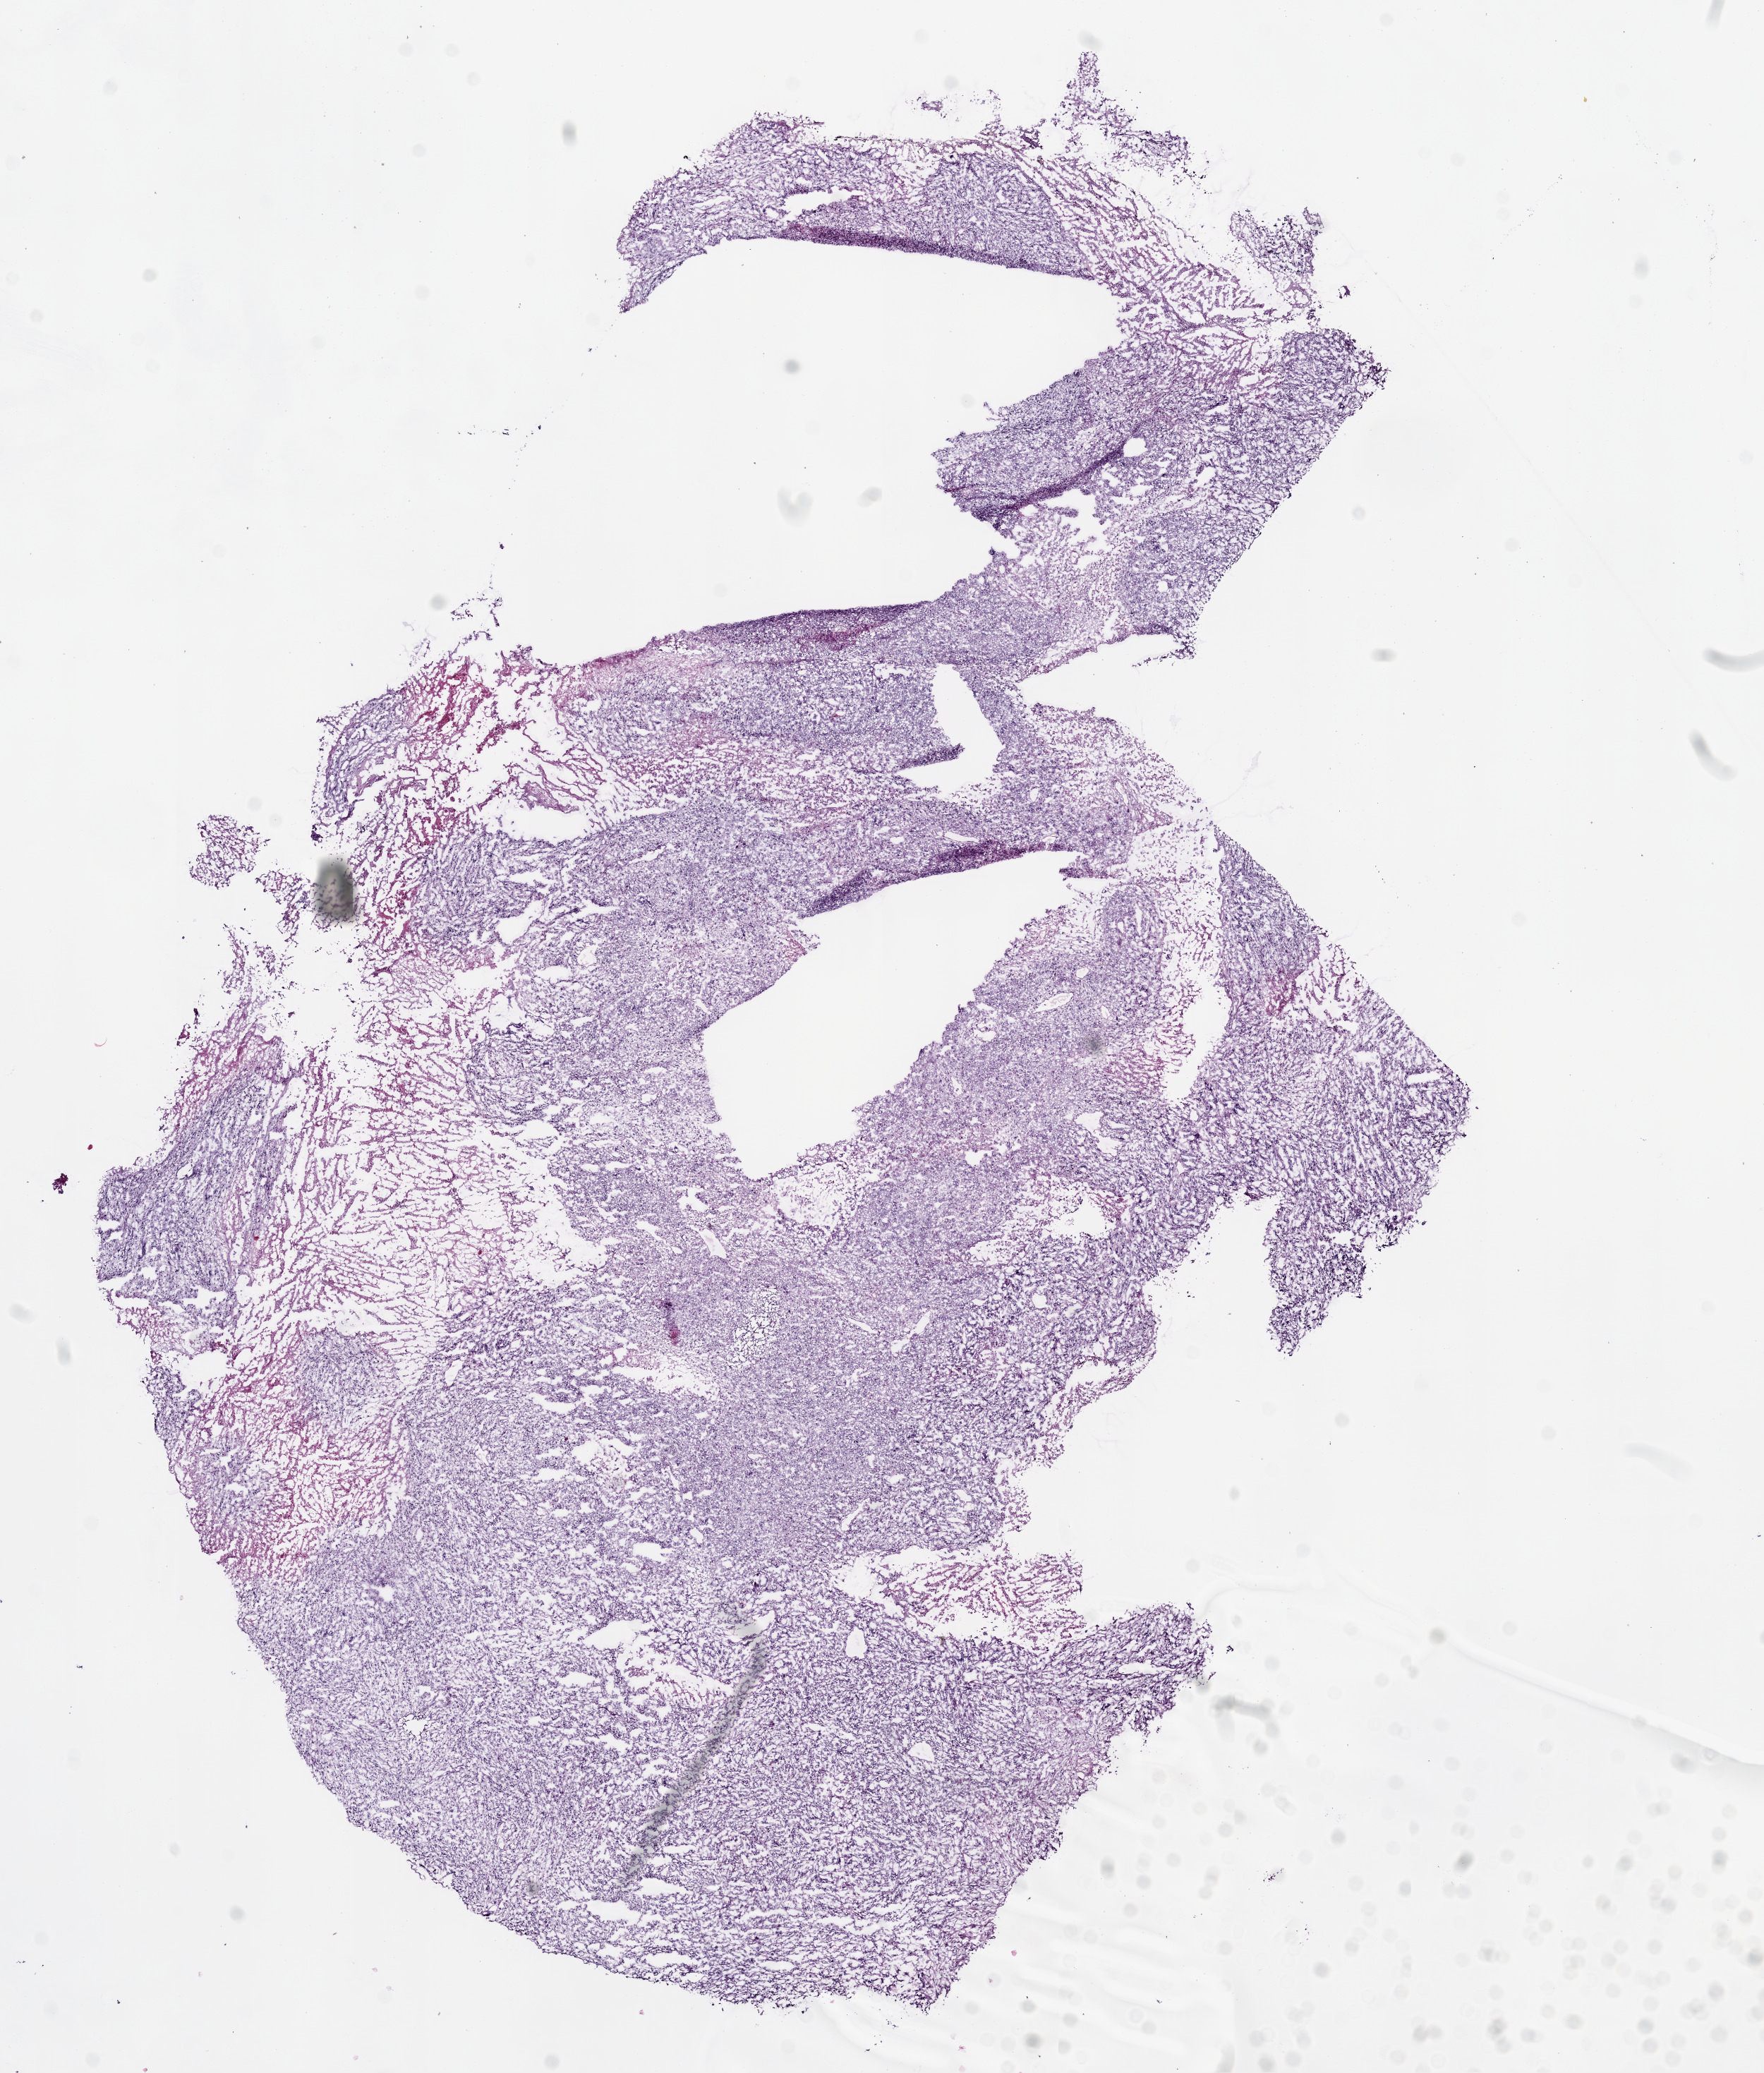
Digitized H&E tissue section (whole slide) — whole scanned area (about 10.0 x 11.8 mm, slide scanned at 20x) shown as a low-resolution overview, frozen section from the bottom of the tissue portion, primary tumour sample from the lung. Female, age 76 years at initial diagnosis. Composition of this section per pathologist review: tumour cells 75%, tumour nuclei 70%, normal cells 0%, stromal cells 5%, necrosis 20%.
- laterality: left
- AJCC pathologic stage: IB
- histologic diagnosis: Squamous cell carcinoma, NOS